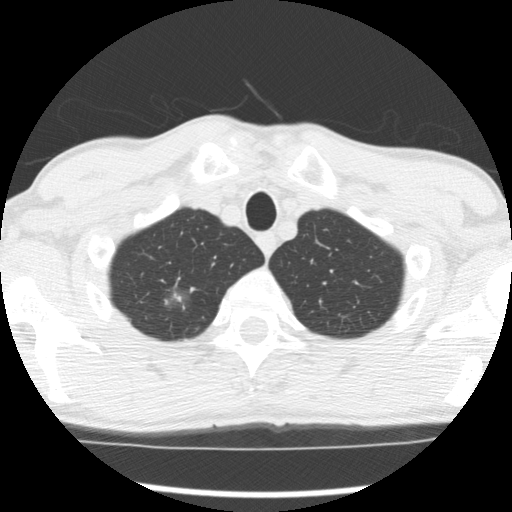
Axial slice from a low-dose chest CT screening exam. Baseline screening round. Lung window (W 1500 / L -600 HU). Slice 29 of 277 in the series. Male participant, aged 66 years at enrolment.
• Expert reader's lesion annotation, bounding box (x1, y1, x2, y2) in pixels: (156, 281, 201, 326).
• The screening reader recorded 4 non-calcified nodules or masses ≥4 mm on this exam; which of them this box marks is not recorded.
• Official screen result: positive, change unspecified: nodule(s) >= 4 mm or enlarging nodule(s), mass(es), or other non-specific abnormalities suspicious for lung cancer.
• Participant outcome: lung cancer diagnosed 503 days after this screen (after the second annual screen) — adenocarcinoma, NOS, right upper lobe, undifferentiated (G4), stage IA (AJCC 6th edition), 20 mm at pathology.